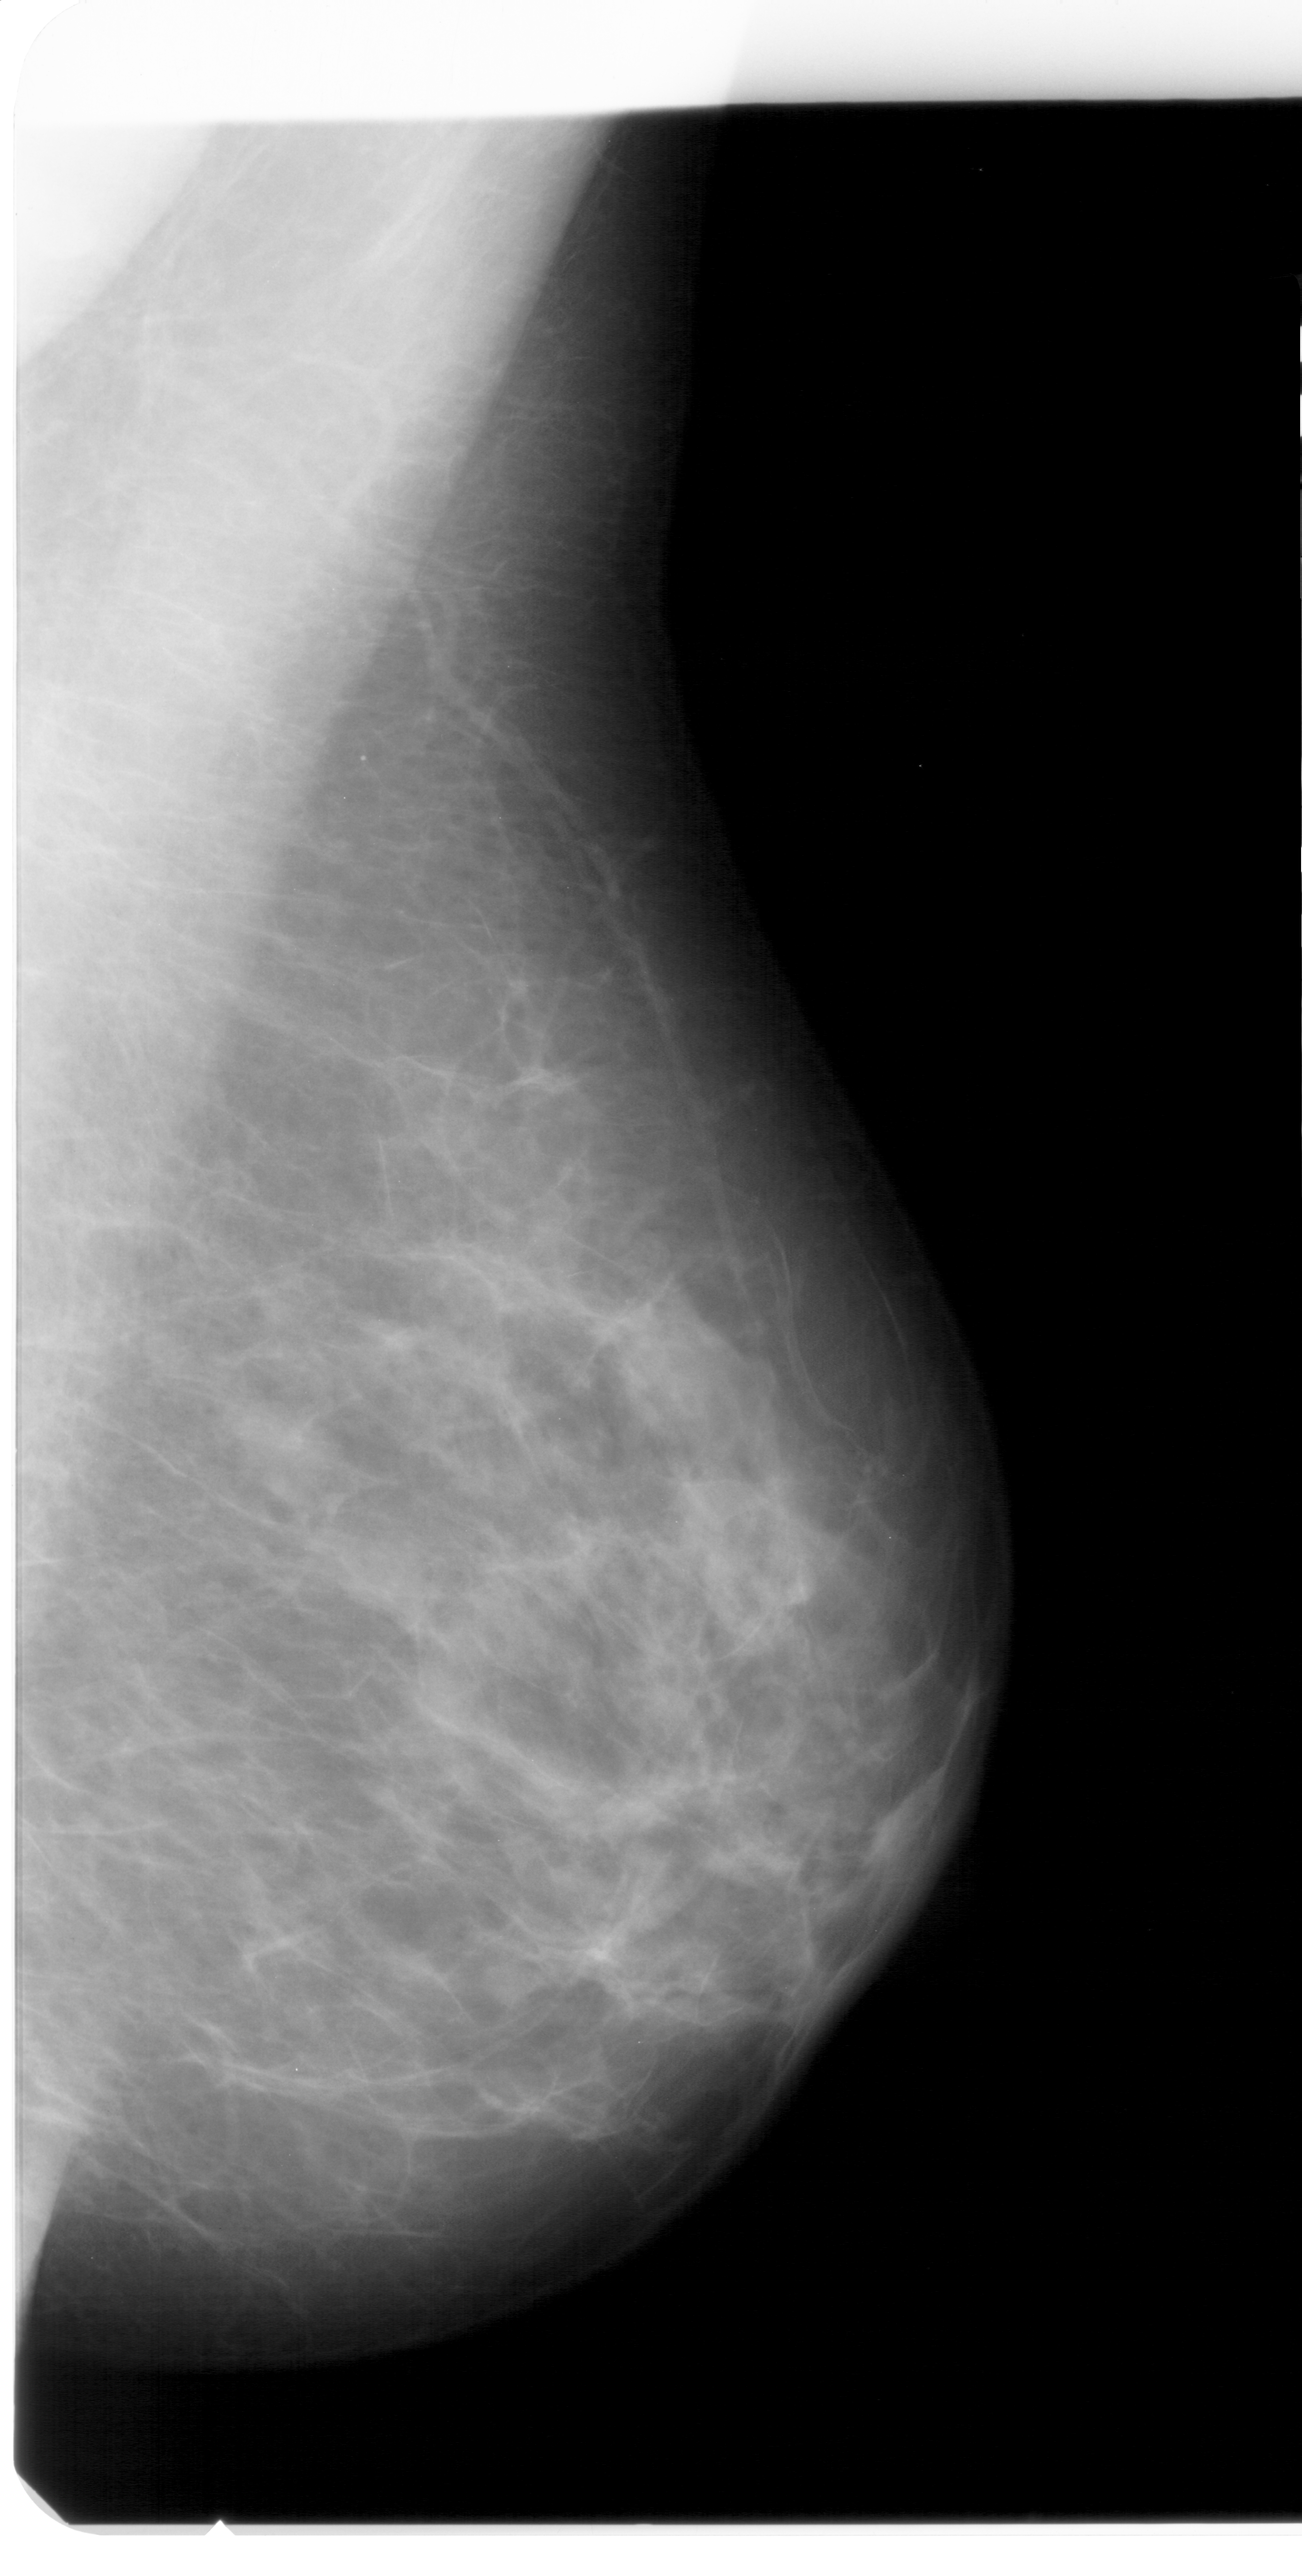
Mammogram (digitized film). Right breast. Mediolateral oblique (MLO) view. BI-RADS breast density category 2 (scale 1–4). 1302 × 2576 image matrix.
Expert-marked regions of interest on this film, with their recorded descriptors:
- mass, shape oval, margins ill defined; BI-RADS assessment category 4; pathology (as recorded): benign: bounding box <228,1400,325,1464> (left, top, right, bottom; pixels)